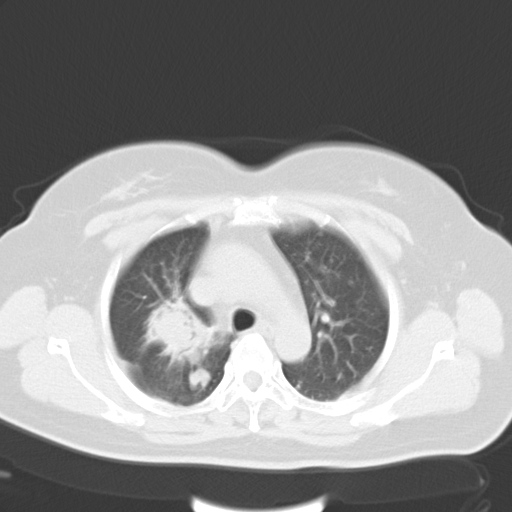
Chest CT, one axial slice; position 23 of 30 along the scan axis; reconstruction kernel B40f; 120 kVp; lung window (W 1500 / L -600 HU); 512 × 512 image matrix, field of view 353 × 353 mm. Patient: female, 50 years. Case-level facts recorded for this patient, not image findings: clinical TNM (as recorded): T2a N0 M1a.
Annotated regions visible in this slice (rectangle marked by the reading radiologist):
- lung tumour (recorded histology: adenocarcinoma): box from (x=138, y=300) to (x=221, y=365) px